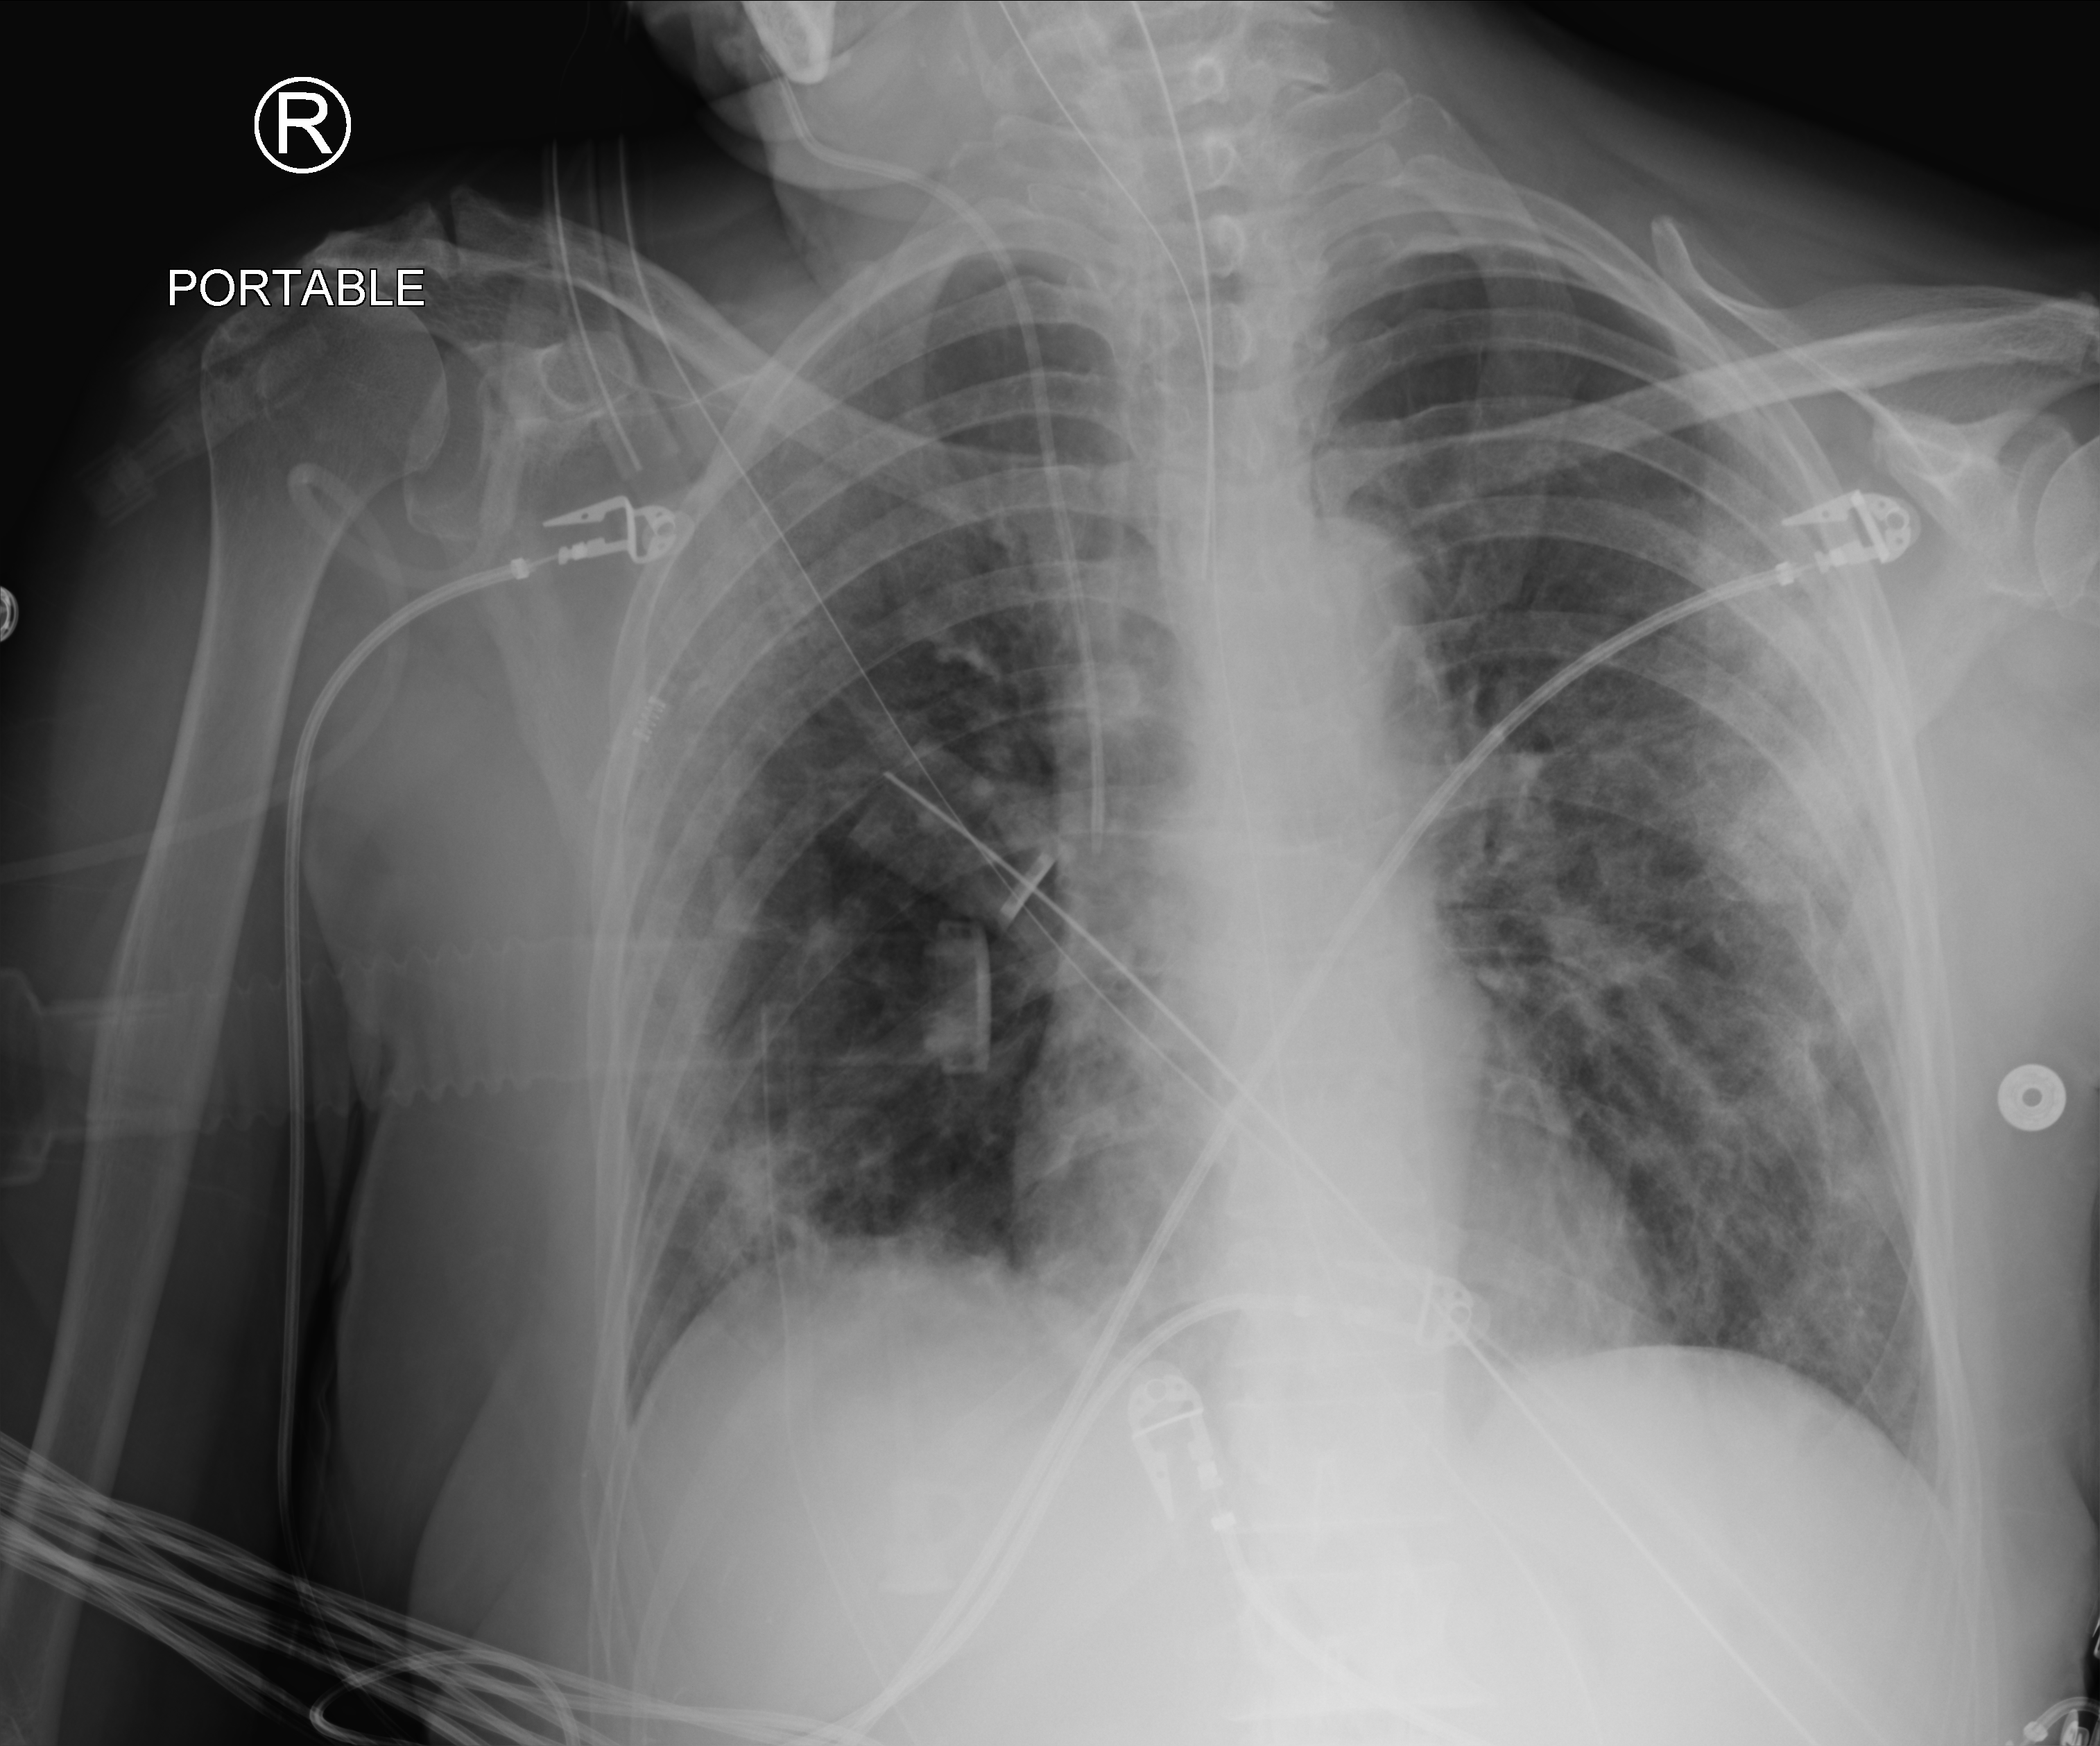
Bedside chest radiograph (computed radiography); anteroposterior (AP) projection. Female patient hospitalised with COVID-19, age 60–74 years.
From the hospital-stay record, not from the radiograph (when in the stay this image was taken is not recorded):
- mechanically ventilated during this hospital stay: yes